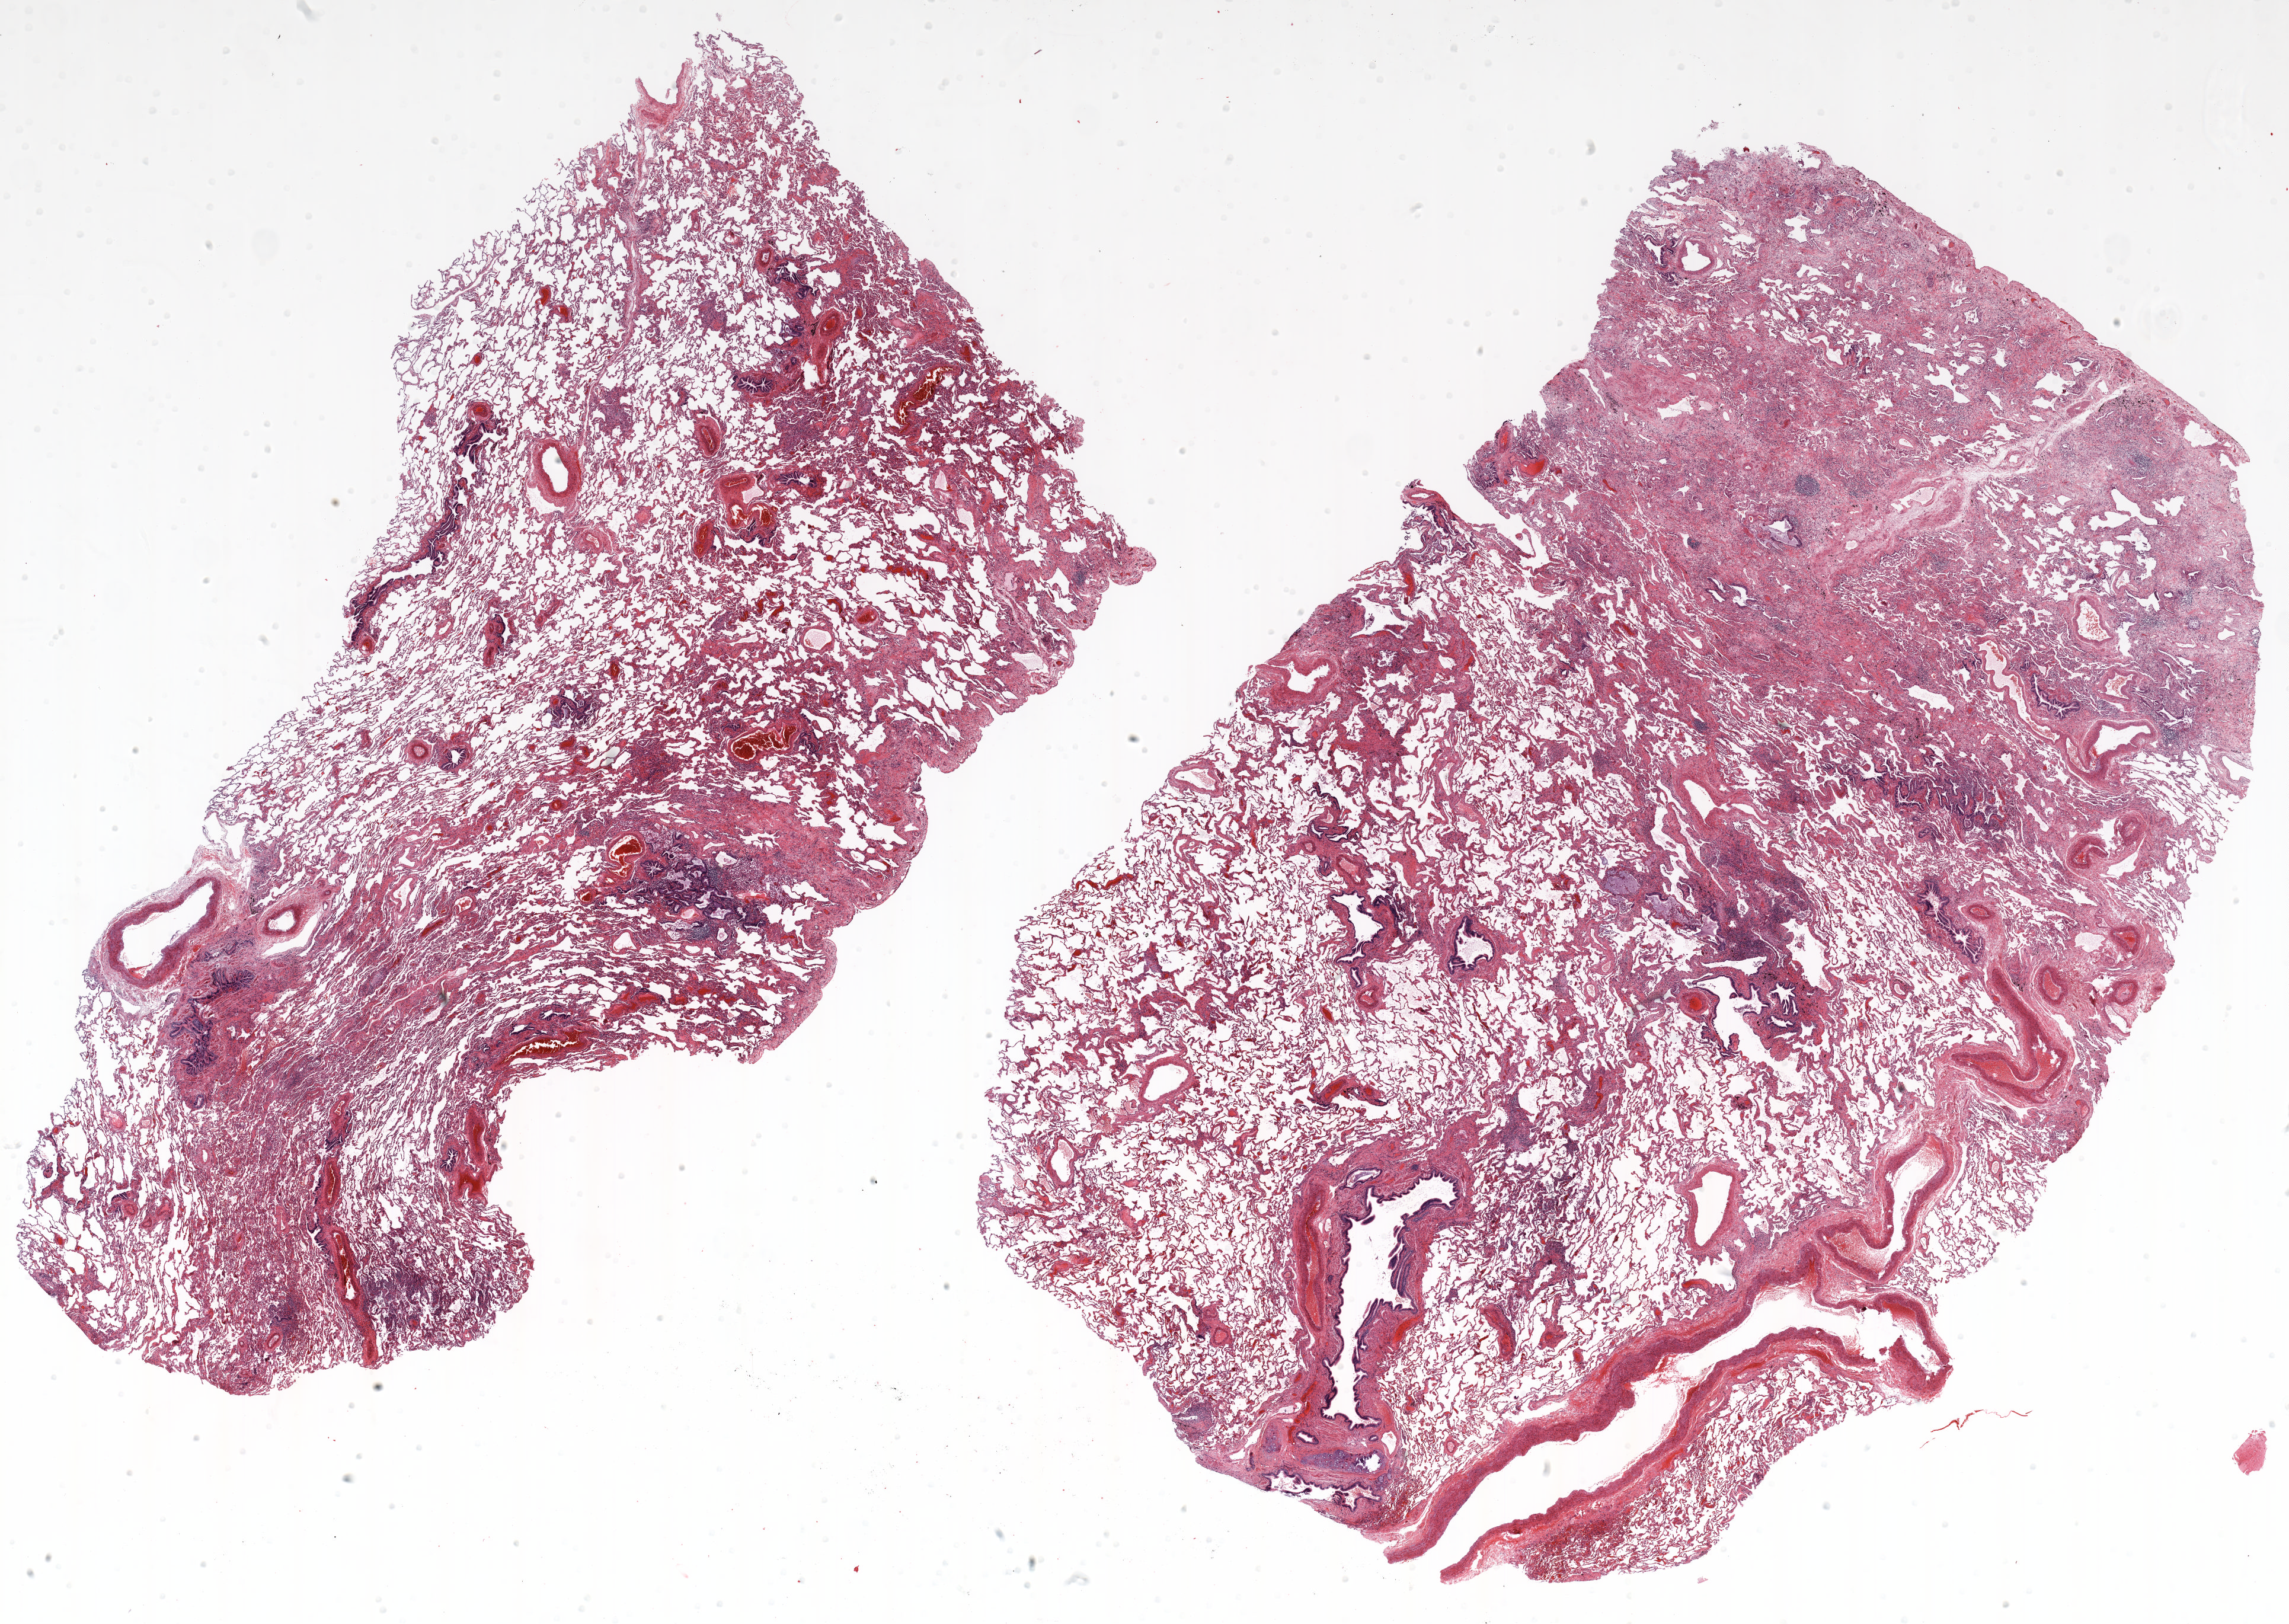
H&E whole-slide image — shown as a low-resolution overview of the whole scanned area (about 31.0 x 22.0 mm, acquisition: 20x scan); formalin-fixed paraffin-embedded (FFPE) section; lung. Male, age 61 at enrolment. Grade: poorly differentiated (G3).
* primary tumour location (clinical record): left lower lobe
* stage (AJCC 6th edition): IA
* tumour size (pathology): 17 mm
* participant's lung-cancer diagnosis: Adenocarcinoma, NOS (ICD-O-3 8140/3)